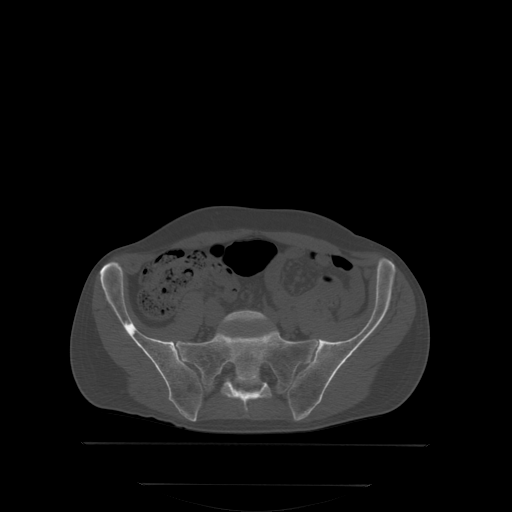
CT including the spine, one axial slice; slice 83 of 350 in the series (ordered by position); bone window (W 1800 / L 400 HU); 2.5 mm slice thickness; 512 × 512 image matrix, field of view 500 × 500 mm. Patient: male, 58 years. From the clinical record (not read from this slice): primary cancer: prostate; vertebrae with lytic lesions (as recorded): L1.
Outlined on this slice (semi-automatically segmented with operator editing):
- L5 vertebra: bounding box (x1, y1, x2, y2) in pixels: (222, 310, 267, 323)